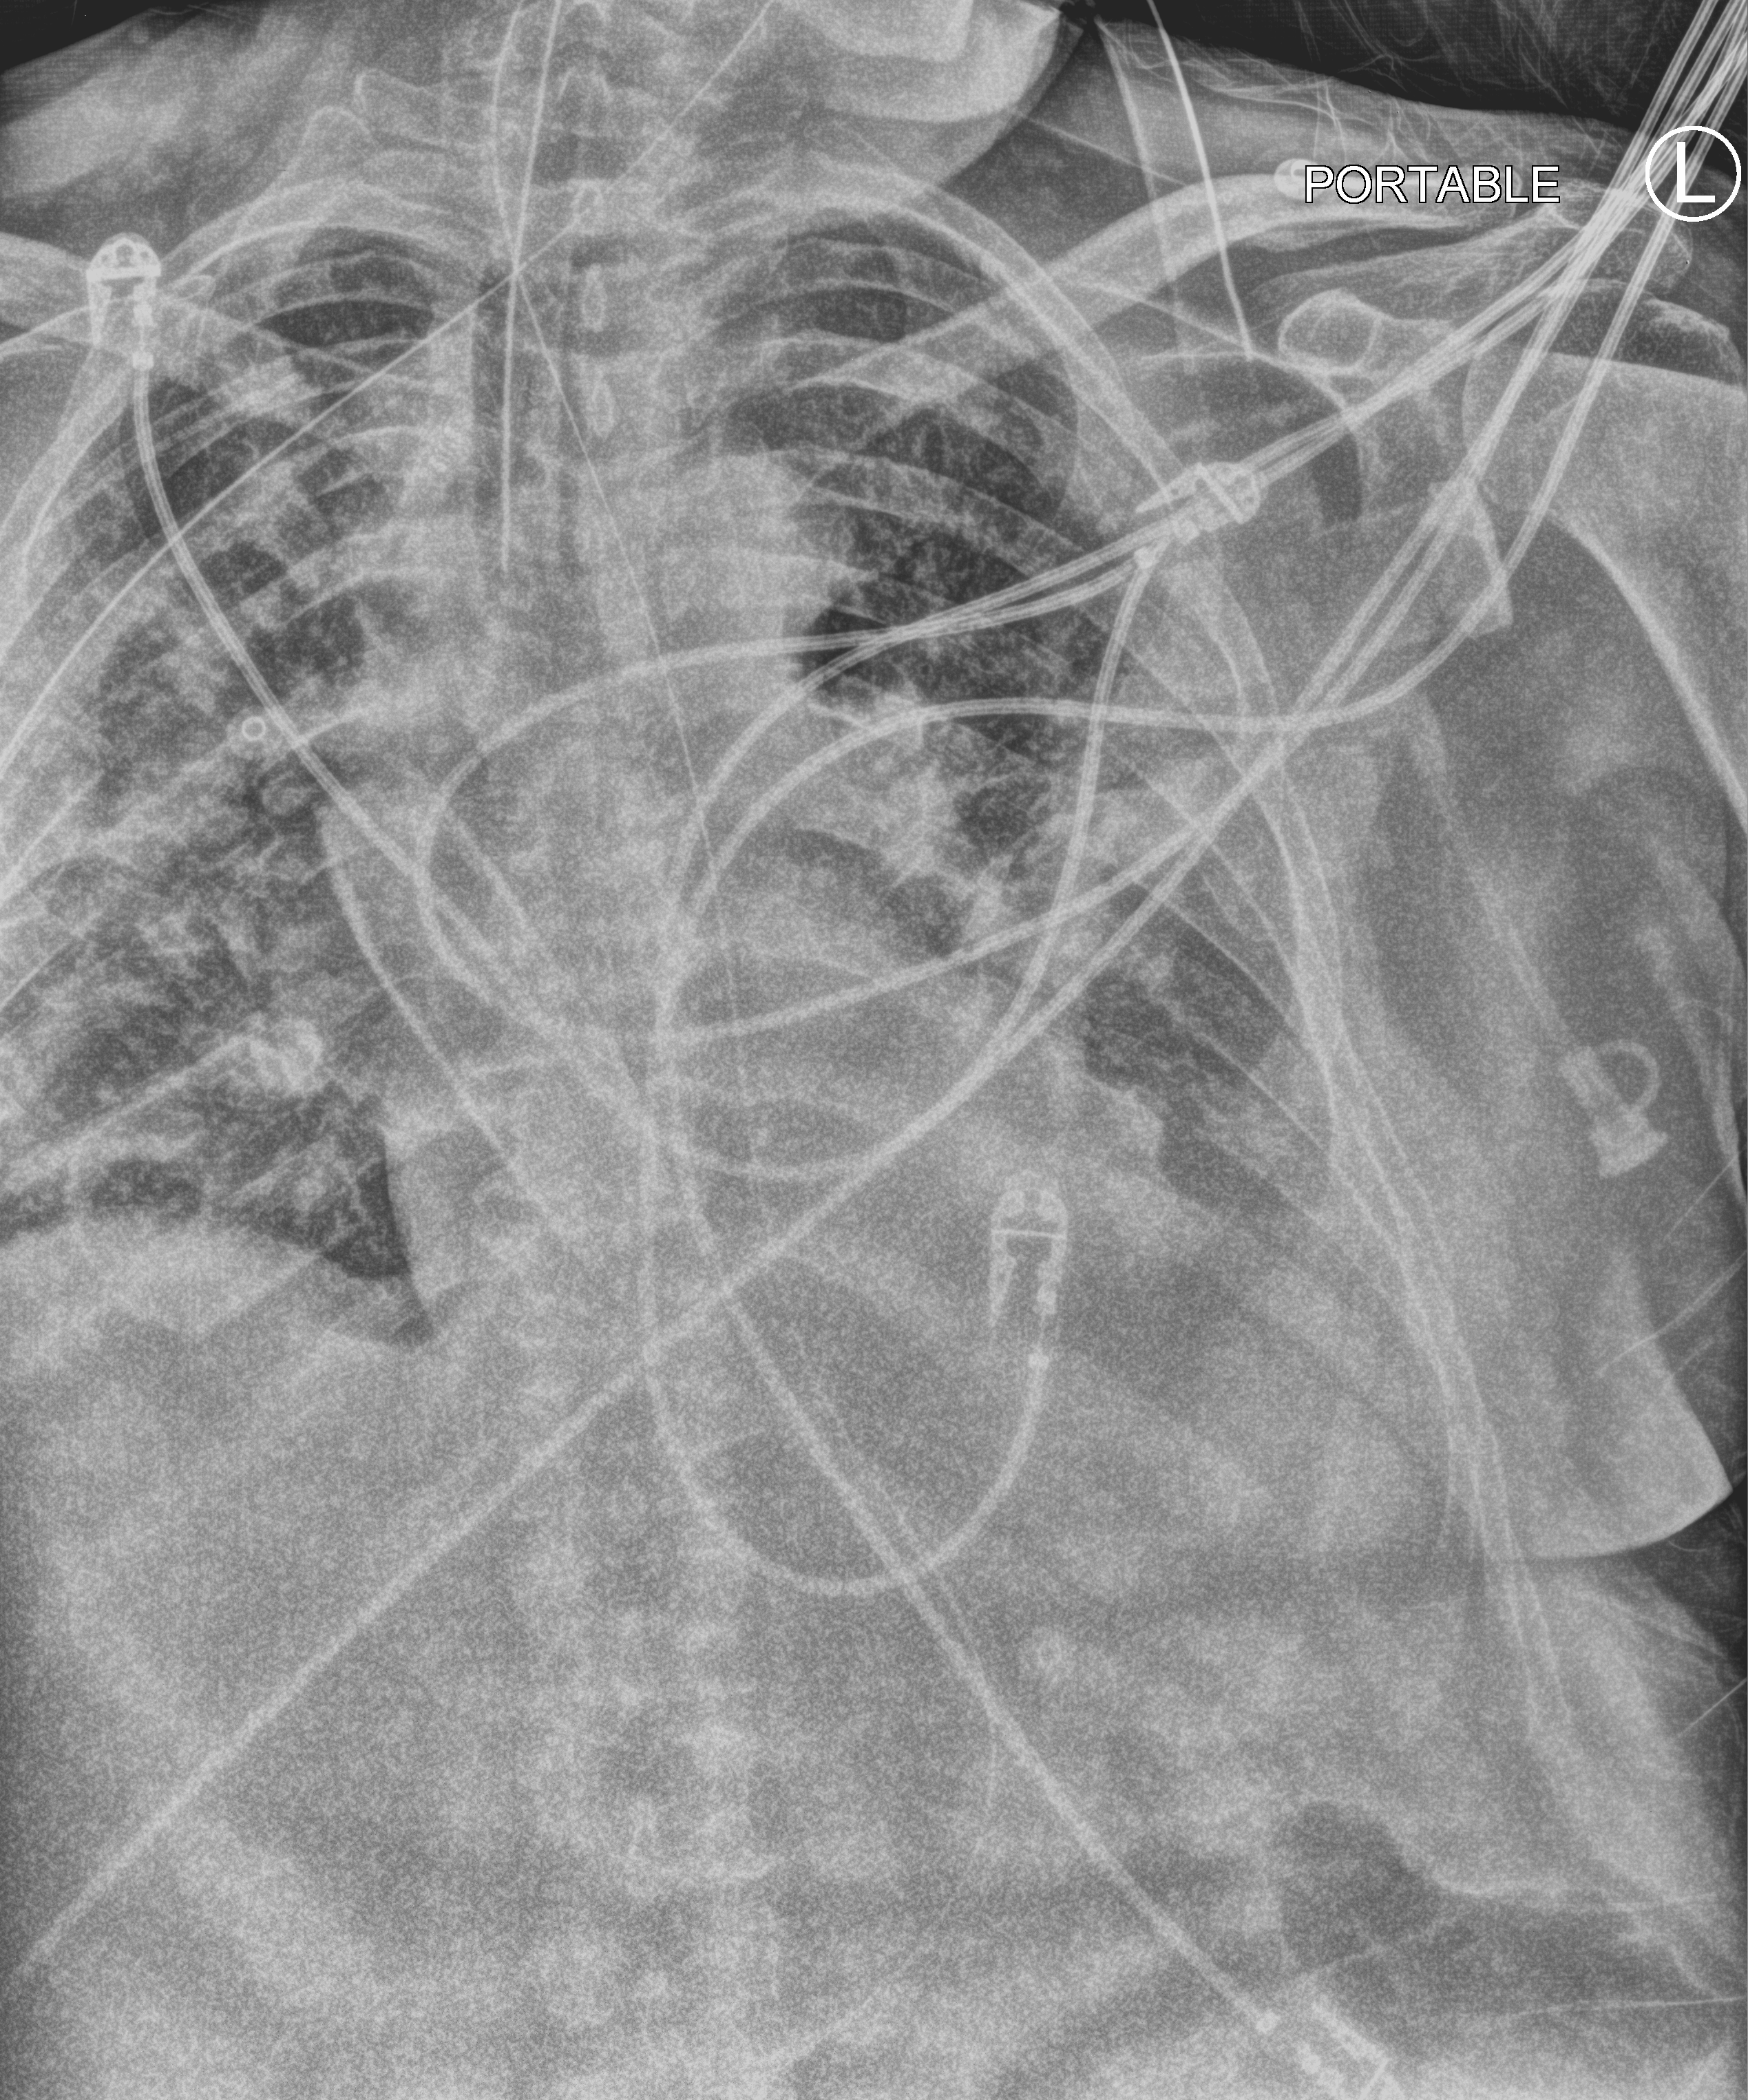
Bedside chest radiograph (computed radiography); anteroposterior (AP) projection. Patient hospitalised with COVID-19; male, aged 60–74 years.
Admission-level facts for this patient (not findings on this image; timing relative to this image not recorded): admitted to intensive care during this hospital stay: yes; length of hospital stay: 24 days.